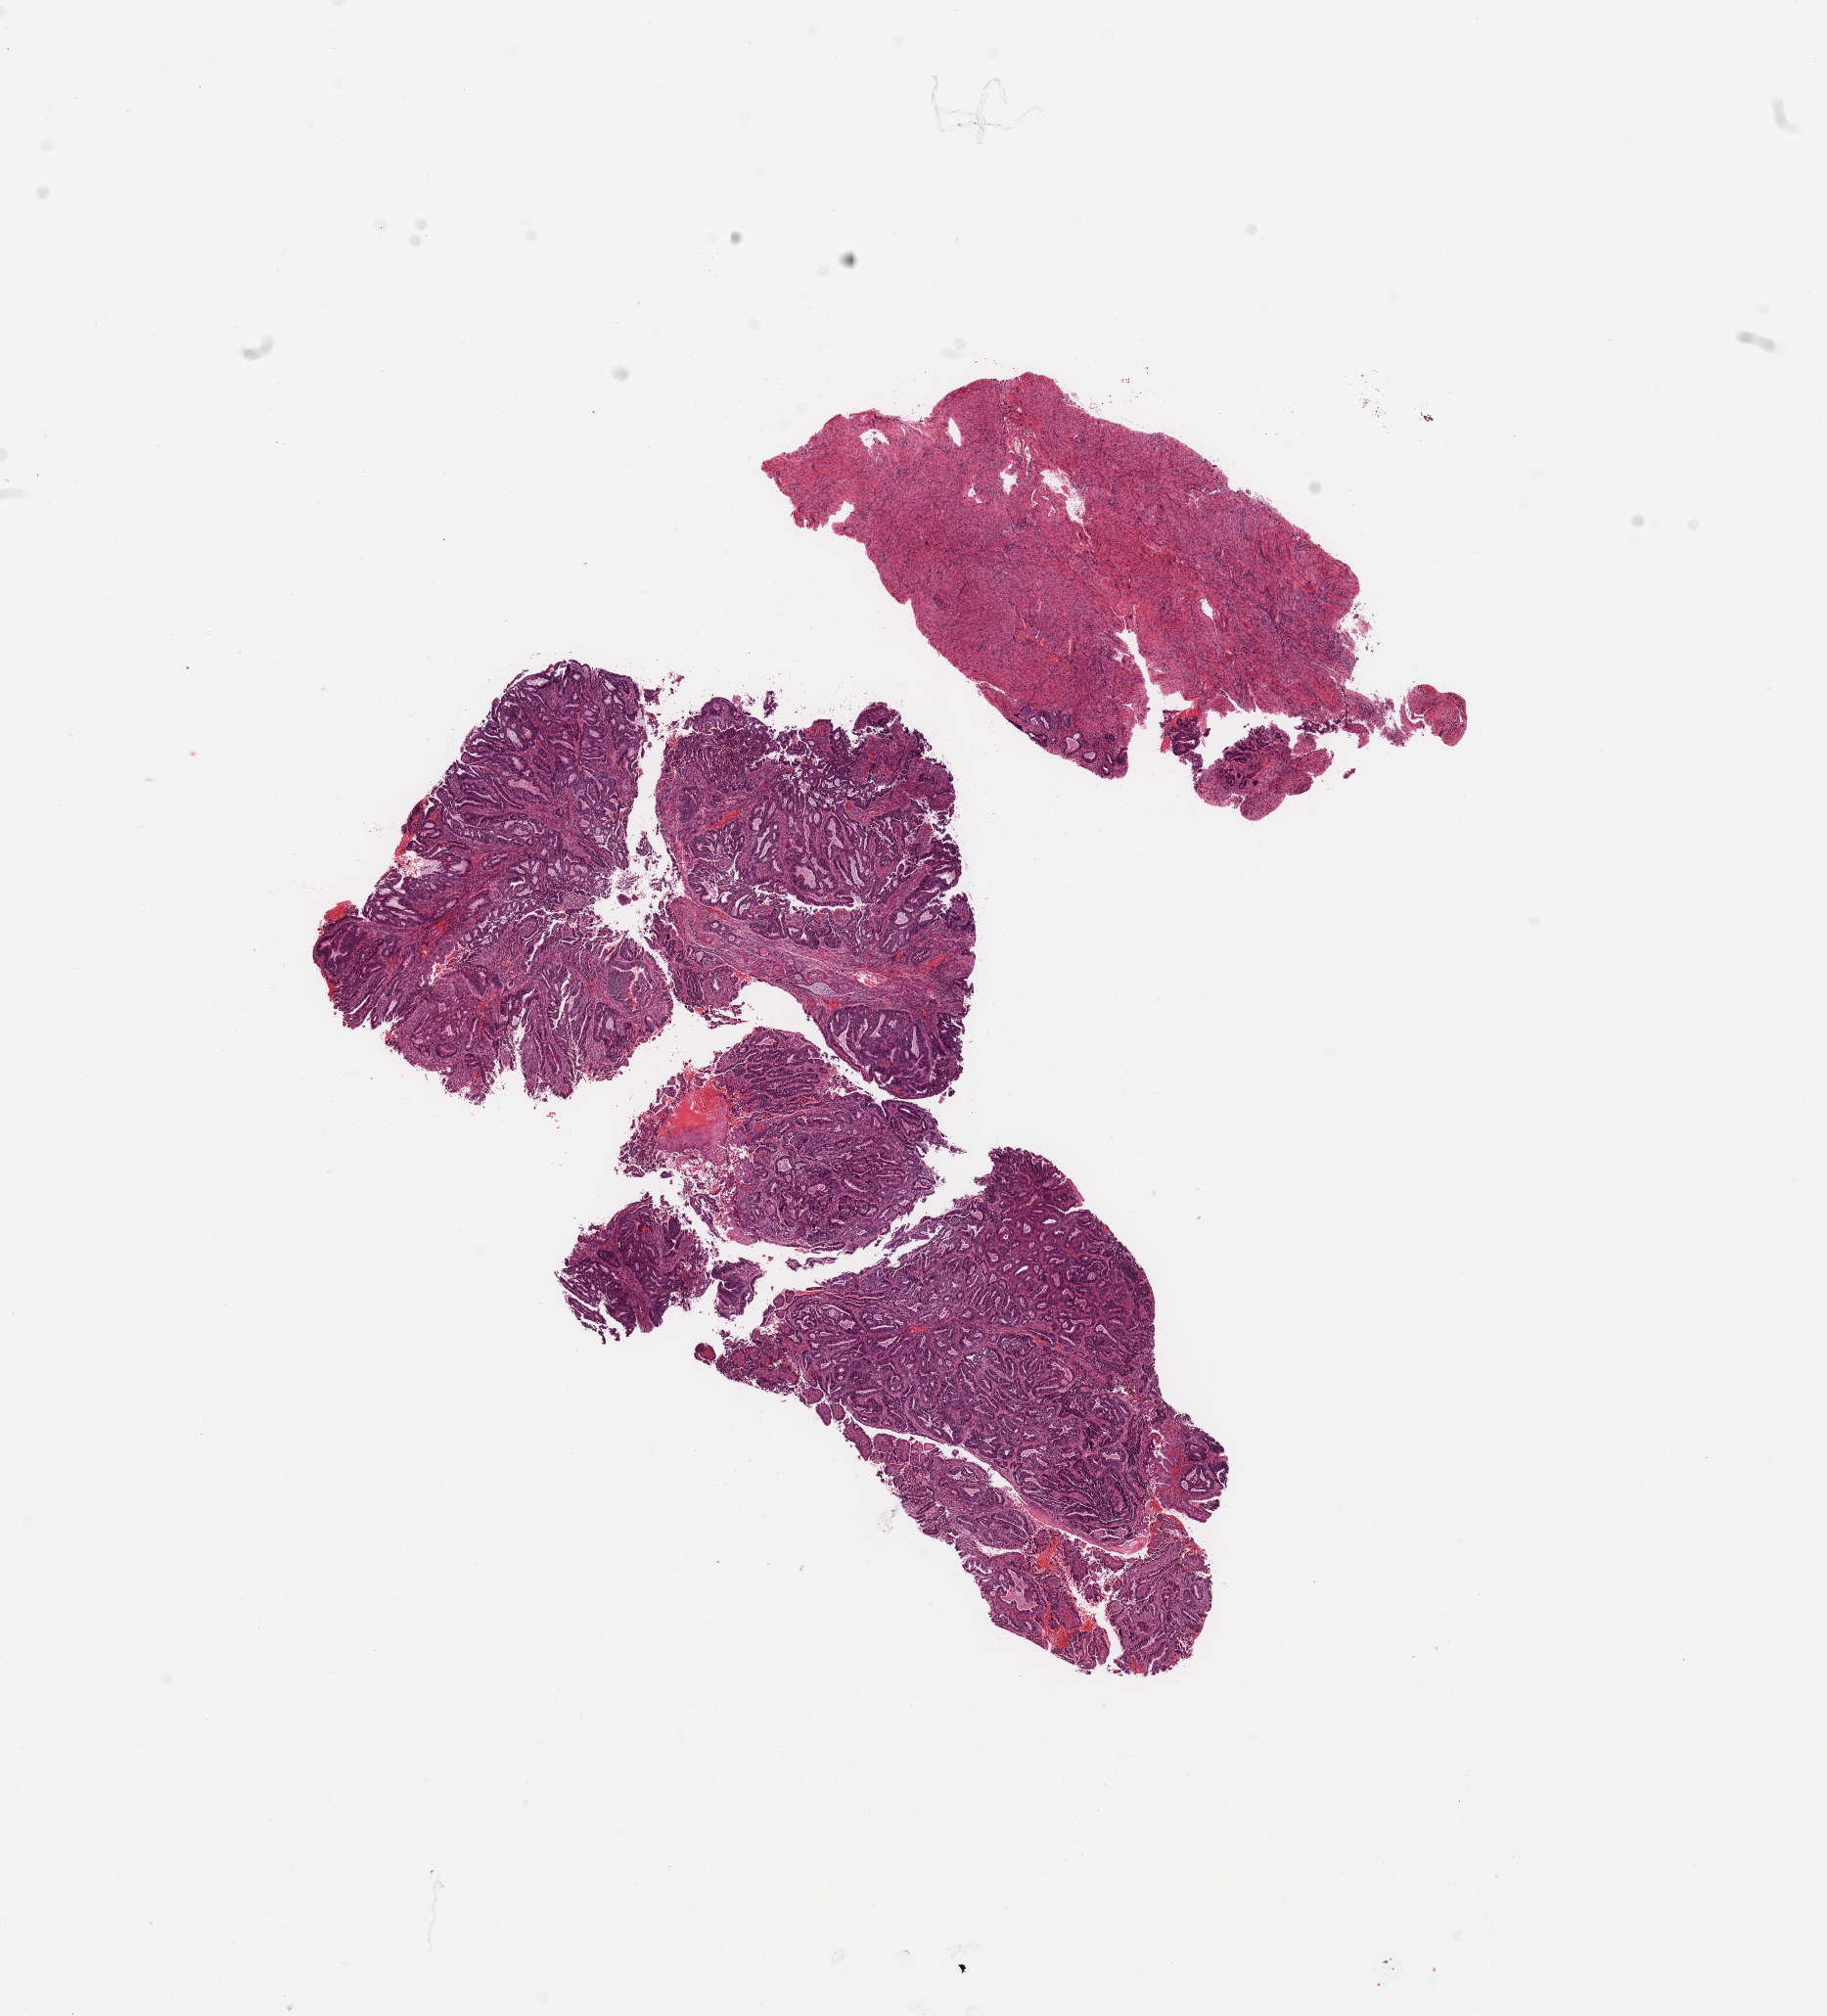
Whole-slide histology image, Hematoxylin and eosin (H&E) stained — a low-resolution overview of the entire scanned area, about 14.8 x 16.3 mm. Tumour tissue sample, sampled site: uterus. Patient: female, age 66 years. Histologic grade: G2 (moderately differentiated). Slide review estimates, as recorded: tumour nuclei 80%, necrosis 0%.
* AJCC pathologic stage: IA
* diagnosis: Endometrioid adenocarcinoma, NOS